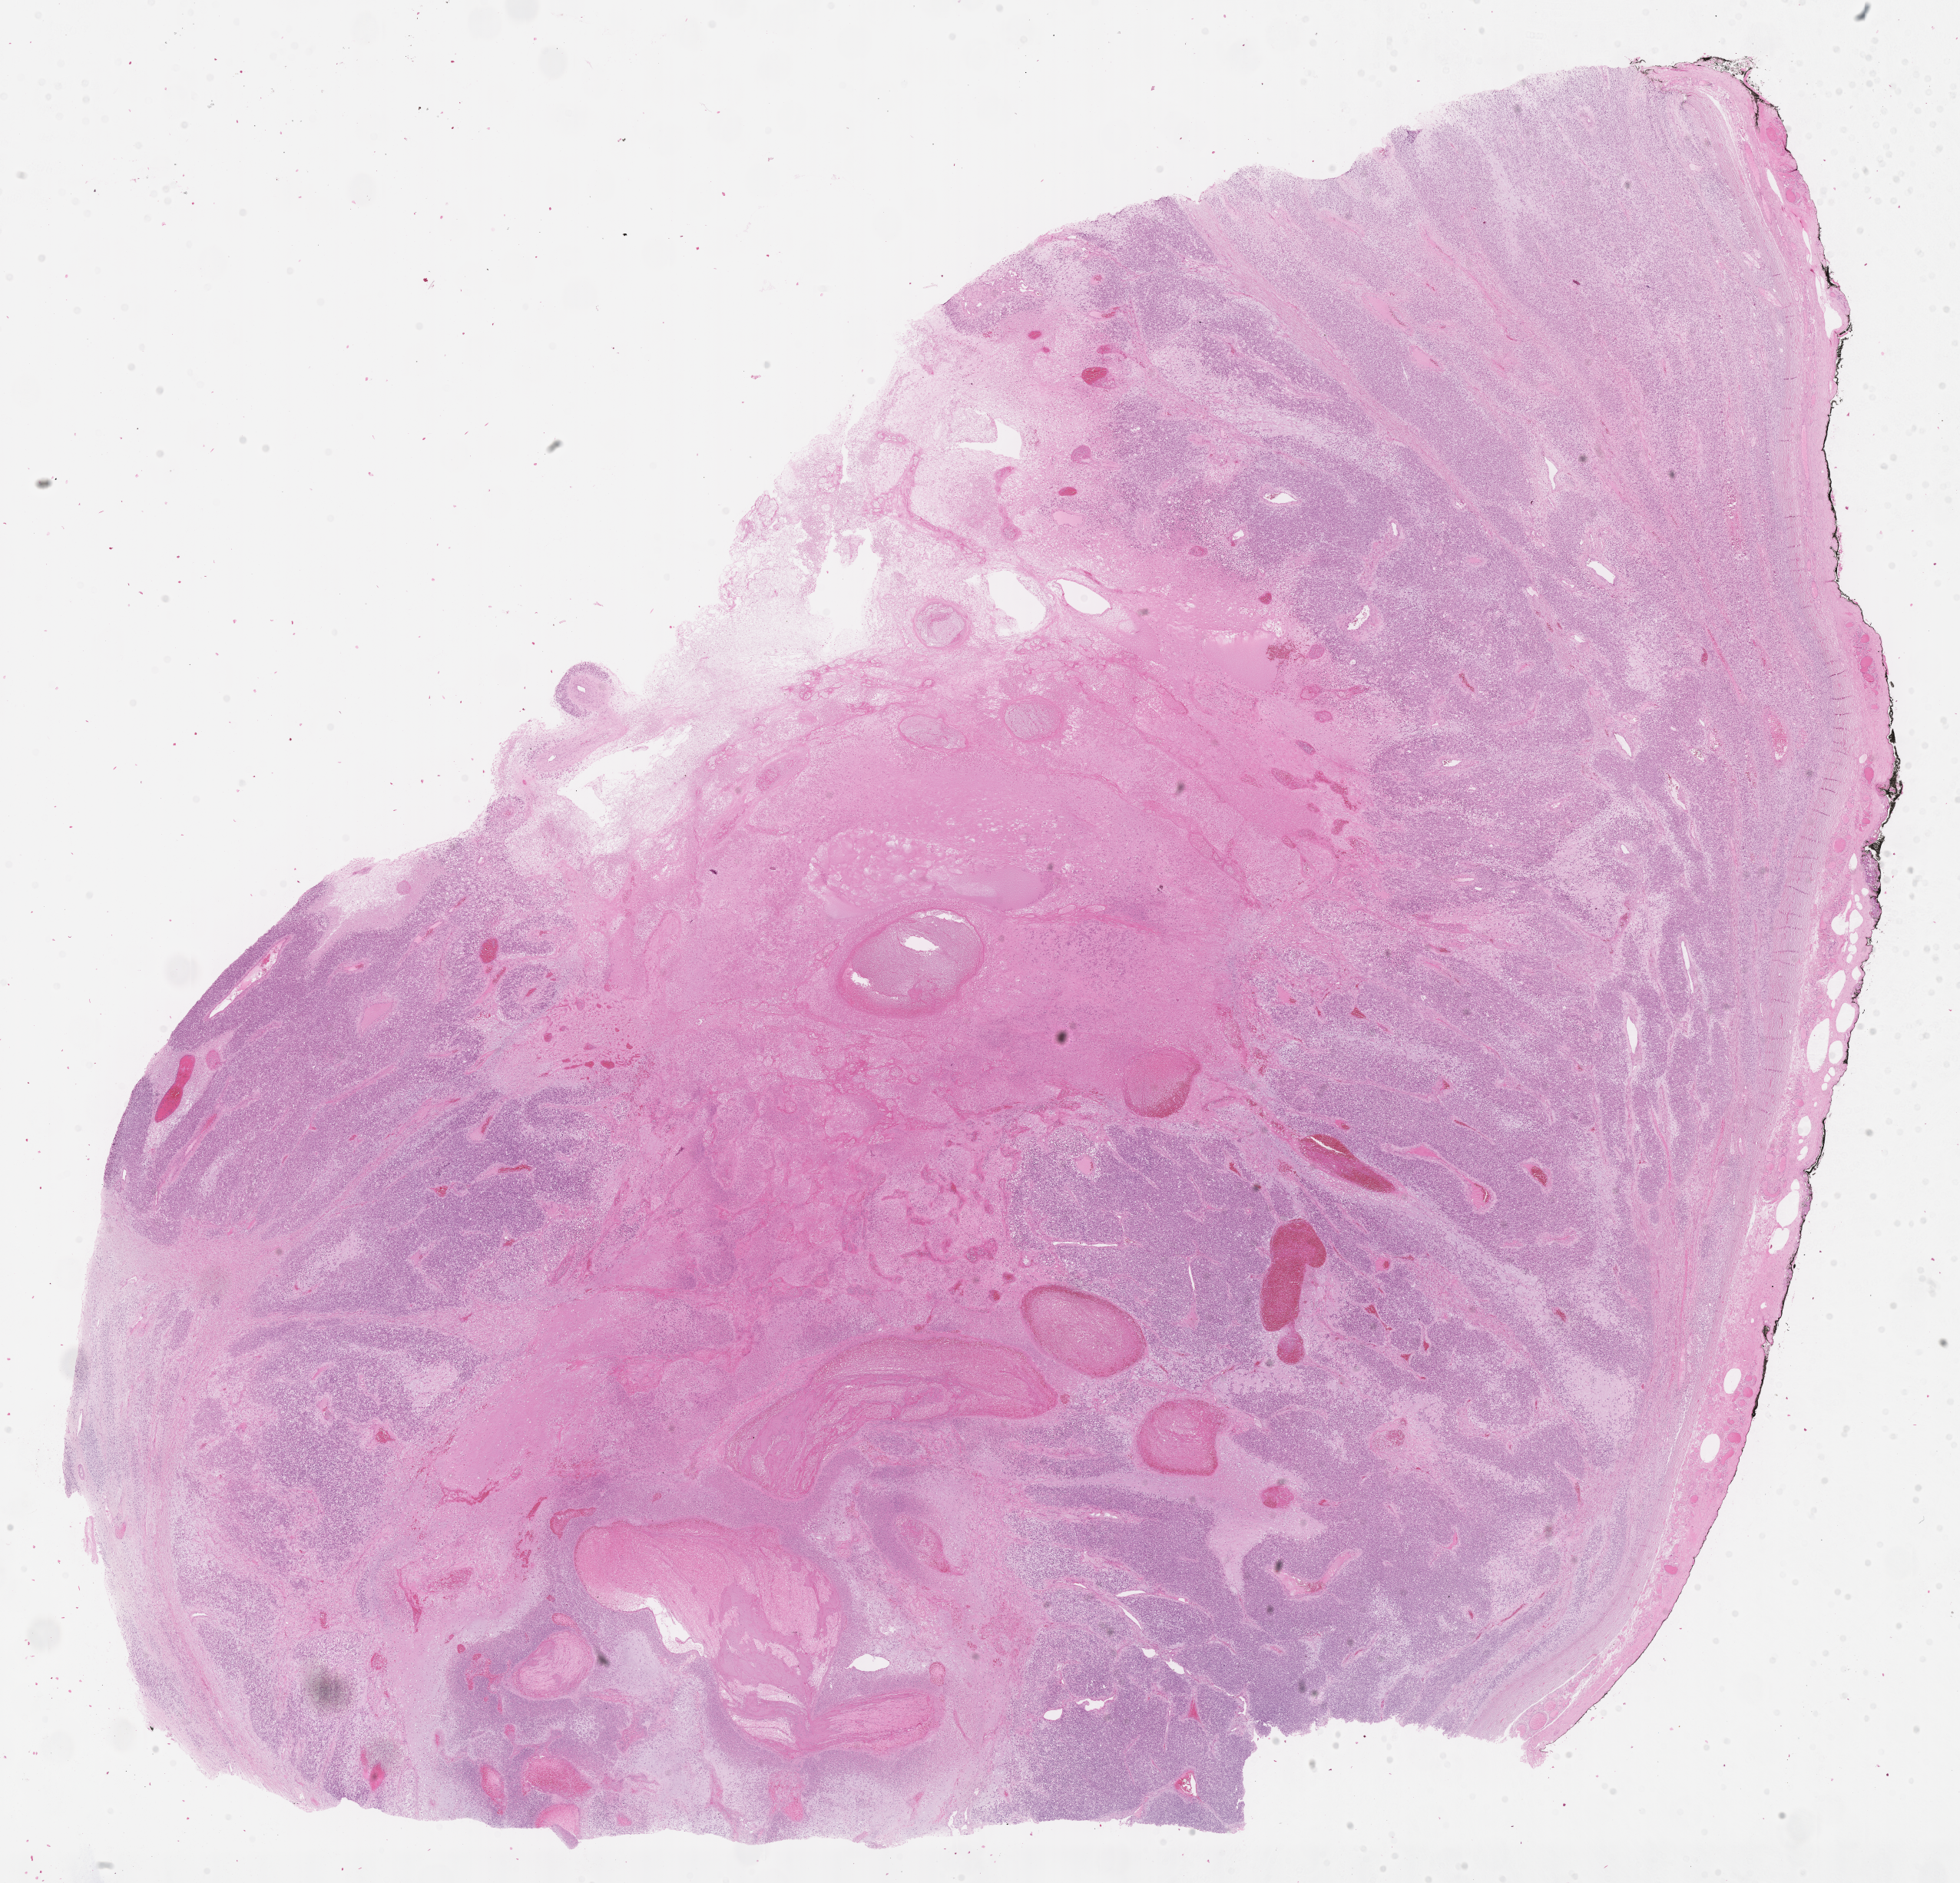
Whole-slide image, H&E stain of tumor tissue — low-resolution overview of the scanned area, about 20.6 x 19.8 mm; formalin-fixed, paraffin-embedded (FFPE) tissue; sample anatomic site: testicle-right. Patient: male, age 15.3 years at diagnosis.
- diagnosis: rhabdomyosarcoma; histological classification: embryonal rhabdomyosarcoma
- stage (as recorded): 1